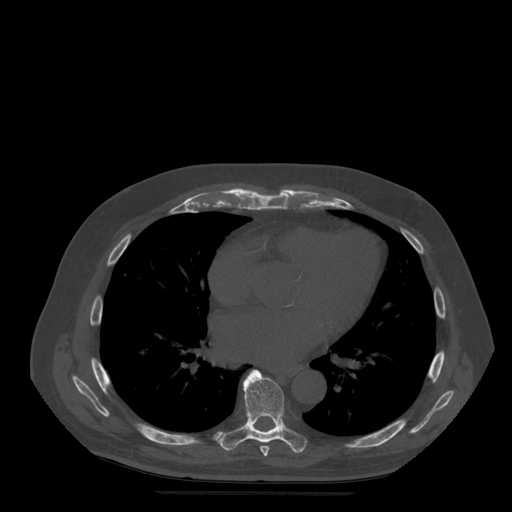
CT including the spine, one axial slice; position 315 of 522 along the scan axis; bone window (W 1800 / L 400 HU); 512 × 512 image matrix, field of view 420 × 420 mm. Patient age 72 years. Case-level facts recorded for this patient, not image findings: primary cancer: prostate.
Structures marked on this image (semi-automatically segmented with operator editing):
- T7 vertebra: bounding box <260,446,270,457> (left, top, right, bottom; pixels)
- T8 vertebra: <218,370,307,454>